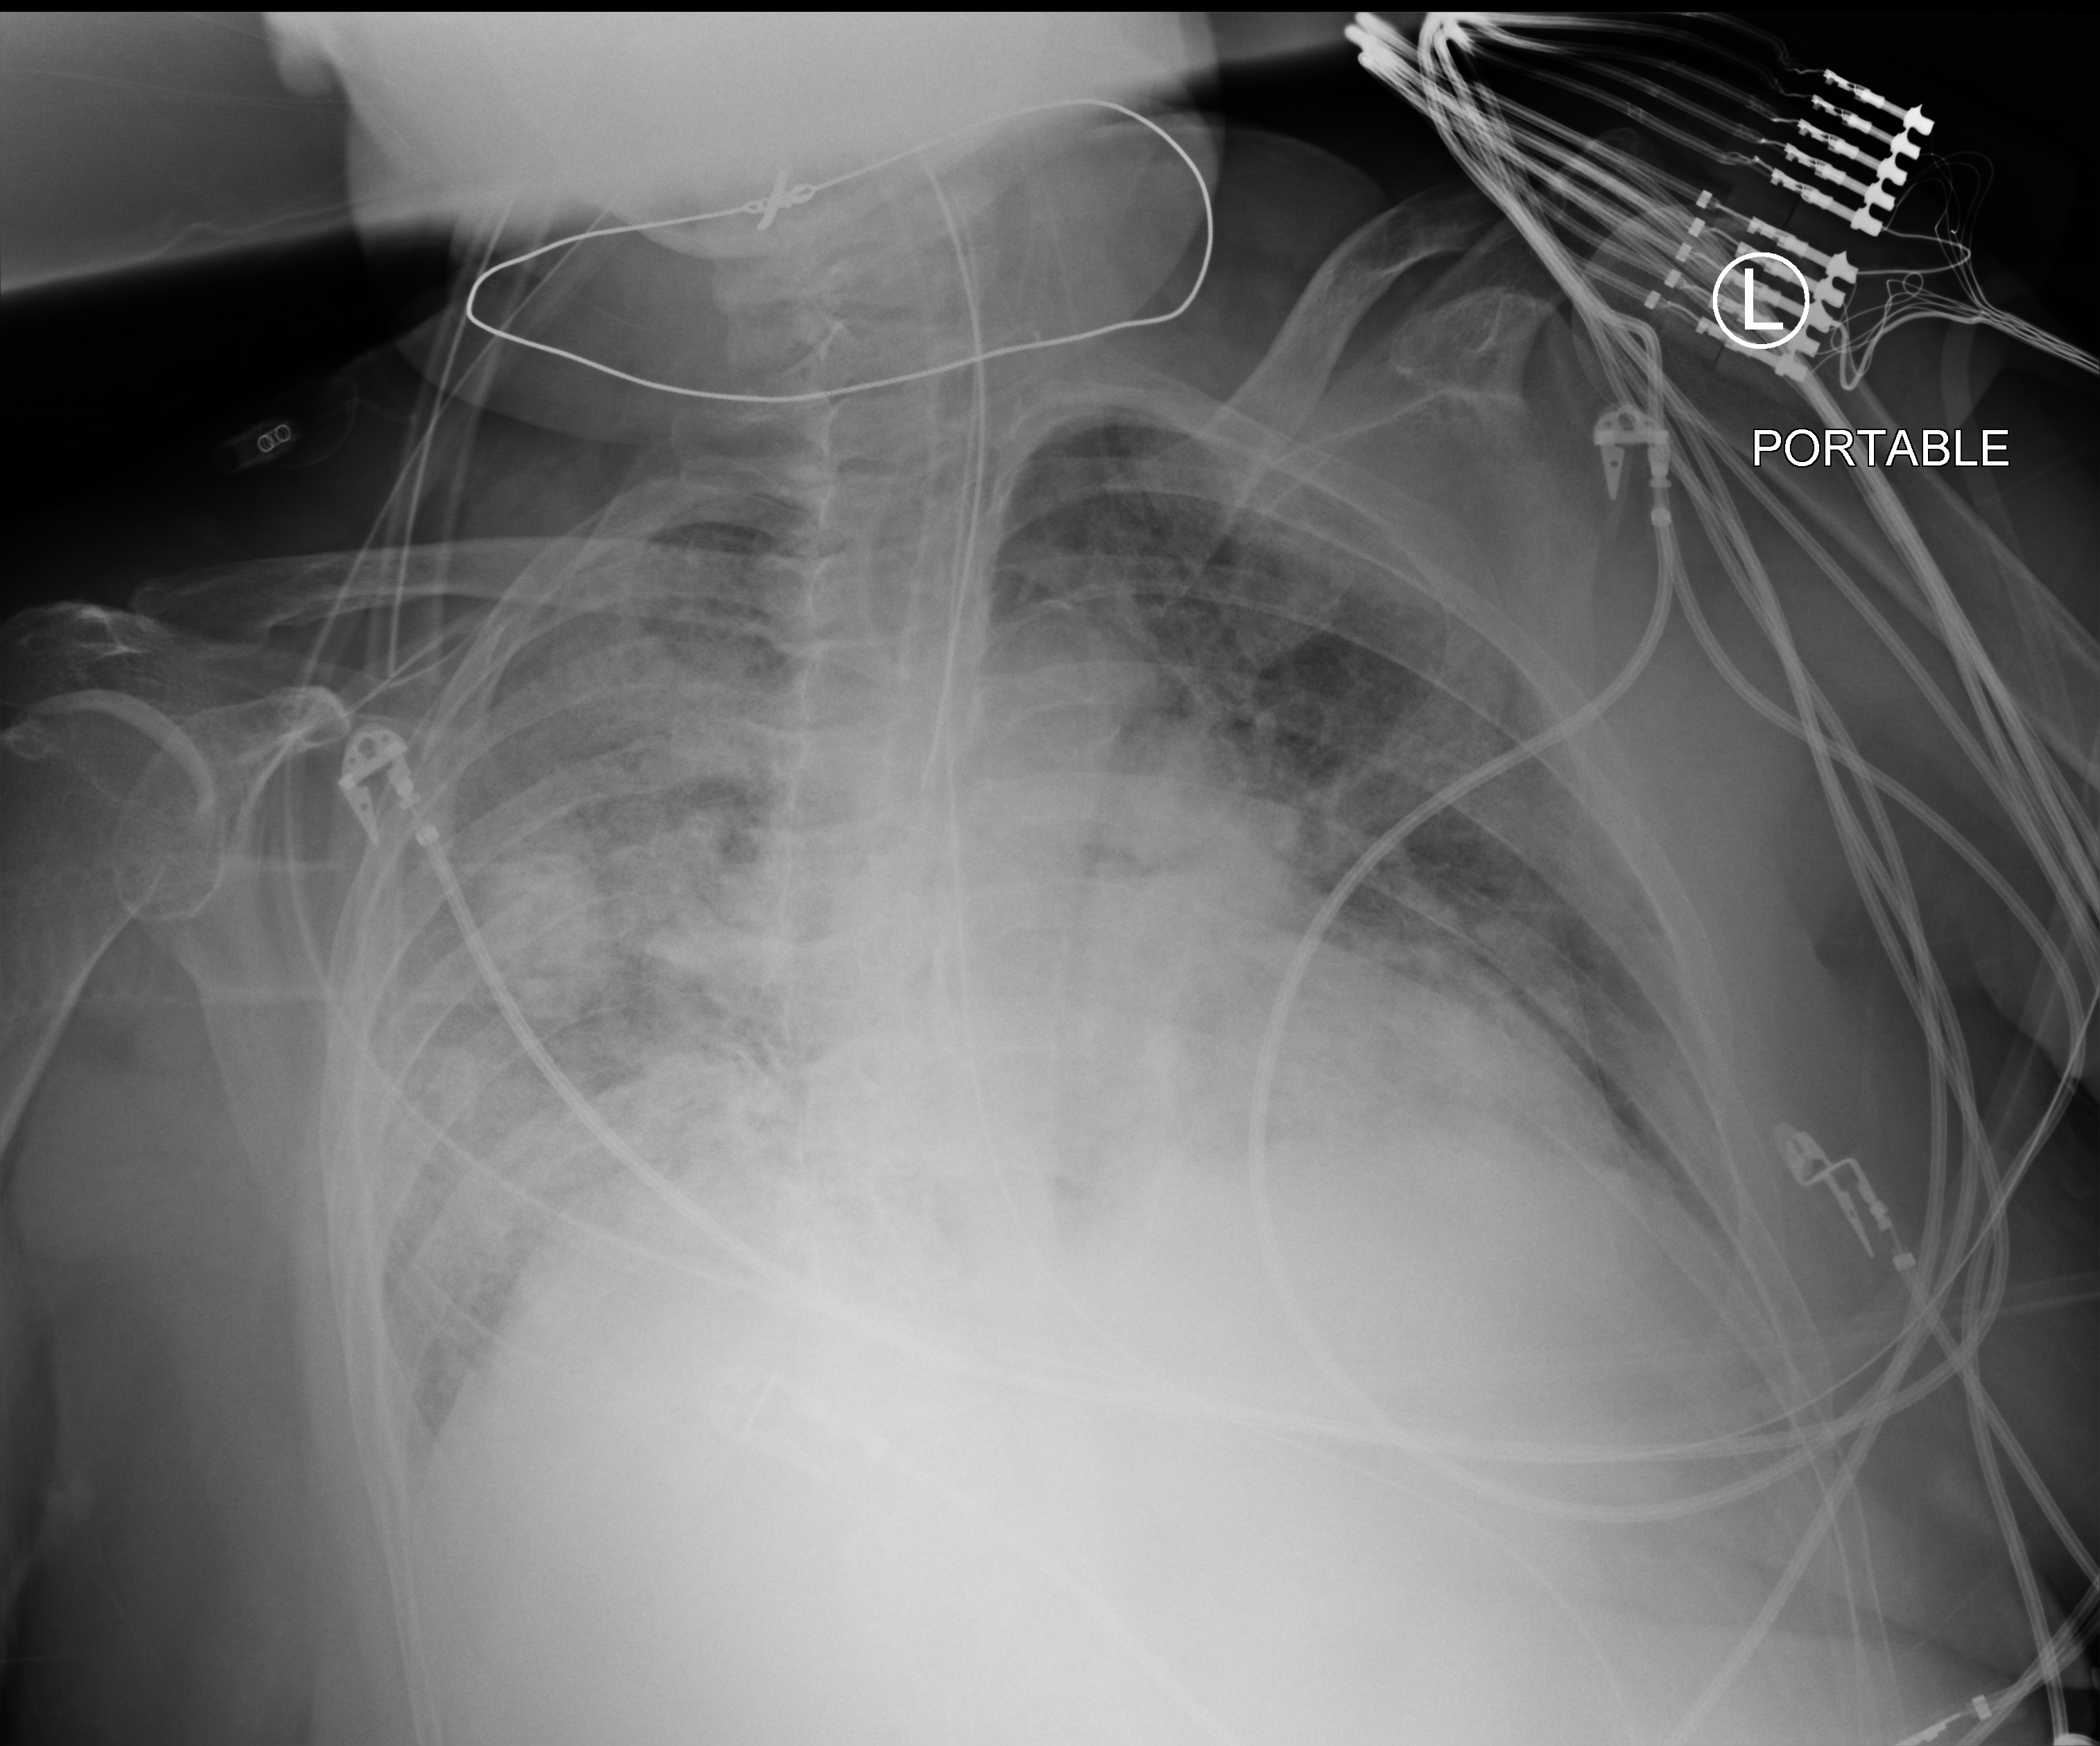
Bedside chest radiograph (computed radiography); anteroposterior (AP) projection. Female patient hospitalised with COVID-19, age 75–90 years.
Hospital-stay facts (about this admission, not read from this image; timing relative to this image not recorded): admitted to intensive care during this hospital stay: yes; smoking status (admission record): former.